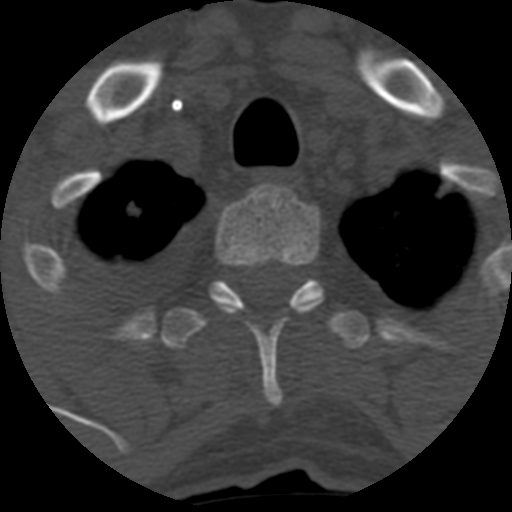
CT including the spine, one axial slice; position 498 of 708 along the scan axis; reconstruction kernel STANDARD; one of 3 acquisitions stored at this slice position; bone window (W 1800 / L 400 HU); 512 × 512 image matrix, field of view 160 × 160 mm. Patient age 55 years. Case-level facts recorded for this patient, not image findings: primary cancer: colon; vertebrae with lytic lesions (as recorded): T12, L1, L5.
Outlined on this slice (semi-automatically segmented with operator editing):
- T2 vertebra: box from (x=213, y=184) to (x=325, y=407) px
- T3 vertebra: (x=161, y=279)–(x=369, y=349)